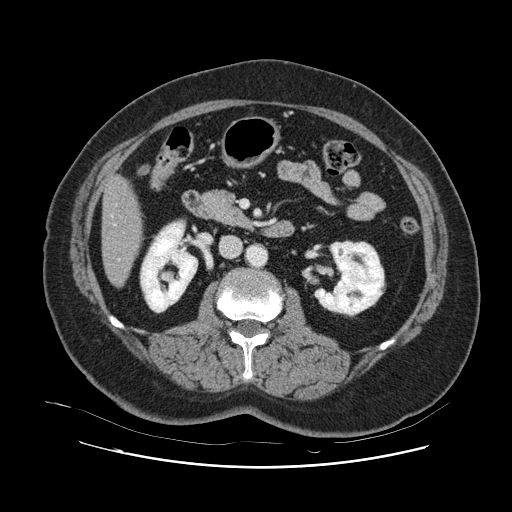
Contrast-enhanced abdominal CT, one axial slice; intravenous contrast given; soft-tissue window (W 400 / L 40 HU); 2.5 mm slice thickness; 512 × 512 image matrix, field of view 391 × 391 mm. Female patient, age 73 years. Case-level facts recorded for this patient, not image findings: diagnosis: colorectal cancer liver metastases, imaged before liver resection; multiple liver metastases: no; largest metastasis: 7 cm; chemotherapy before resection: yes.
Annotated regions visible in this slice (manually delineated by an expert):
- hepatic veins: bounding box (x1, y1, x2, y2) in pixels: (113, 224, 116, 226)
- liver: (103, 179, 142, 285)
- planned liver remnant (the part of the liver to remain after resection): (103, 178, 142, 285)